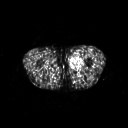
FDG PET of an extremity soft-tissue mass (from a PET/CT study), one axial slice; slice 238 of 311 in the series (ordered by position); 3.27 mm slice thickness; 128 × 128 image matrix. Male patient, age 29 years. Case-level facts recorded for this patient, not image findings: histological type: mixoid liposarcoma; grade: low; site of the primary tumour: left thigh.
Outlined on this slice (expert contour drawn on MRI and transferred to this co-registered scan by the dataset authors):
- gross tumour volume (mass): bounding box (x1, y1, x2, y2) in pixels: (70, 53, 82, 70)